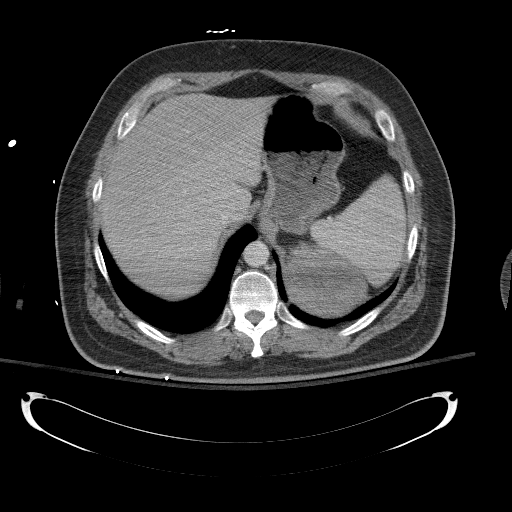
Contrast-enhanced abdominal CT, one axial slice. Position 97 of 154 along the scan axis. Reconstruction kernel B41f. 120 kVp. Intravenous contrast given. Soft-tissue window (W 400 / L 40 HU). 5 mm slice thickness. 512 × 512 image matrix. Patient: male, 43 years. Case-level facts recorded for this patient, not image findings: diagnosis: adrenocortical carcinoma; tumour side: left adrenal; tumour size at pathology: 9.8 cm; Ki-67 index: 30 %; stage (as recorded): 2.
Outlined on this slice (semi-automatically segmented with operator editing):
- mass: box from (x=289, y=242) to (x=366, y=315) px